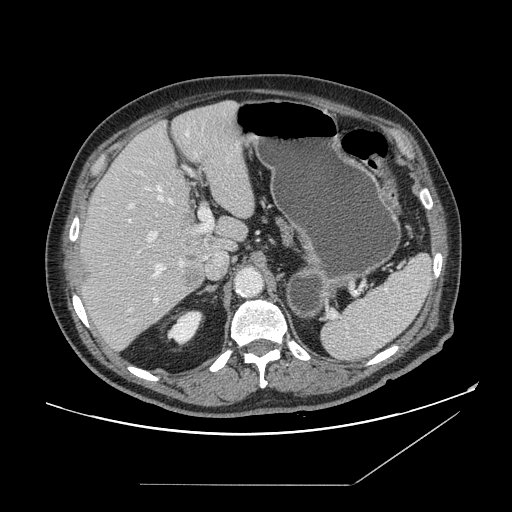
Contrast-enhanced abdominal CT, one axial slice. Position 103 of 166 along the scan axis. 120 kVp. Intravenous contrast given. Soft-tissue window (W 400 / L 40 HU). 512 × 512 image matrix. Male patient, age 80 years. From the clinical record (not read from this slice): diagnosis: colorectal cancer liver metastases, imaged before liver resection.
Annotated regions visible in this slice (manually delineated by an expert):
- hepatic veins: bounding box (x1, y1, x2, y2) in pixels: (129, 132, 189, 311)
- liver: (80, 102, 256, 351)
- planned liver remnant (the part of the liver to remain after resection): (88, 101, 255, 257)
- portal vein (with intrahepatic branches): (130, 204, 213, 301)
- liver metastasis: (84, 274, 198, 283)
- liver metastasis: (185, 270, 201, 287)